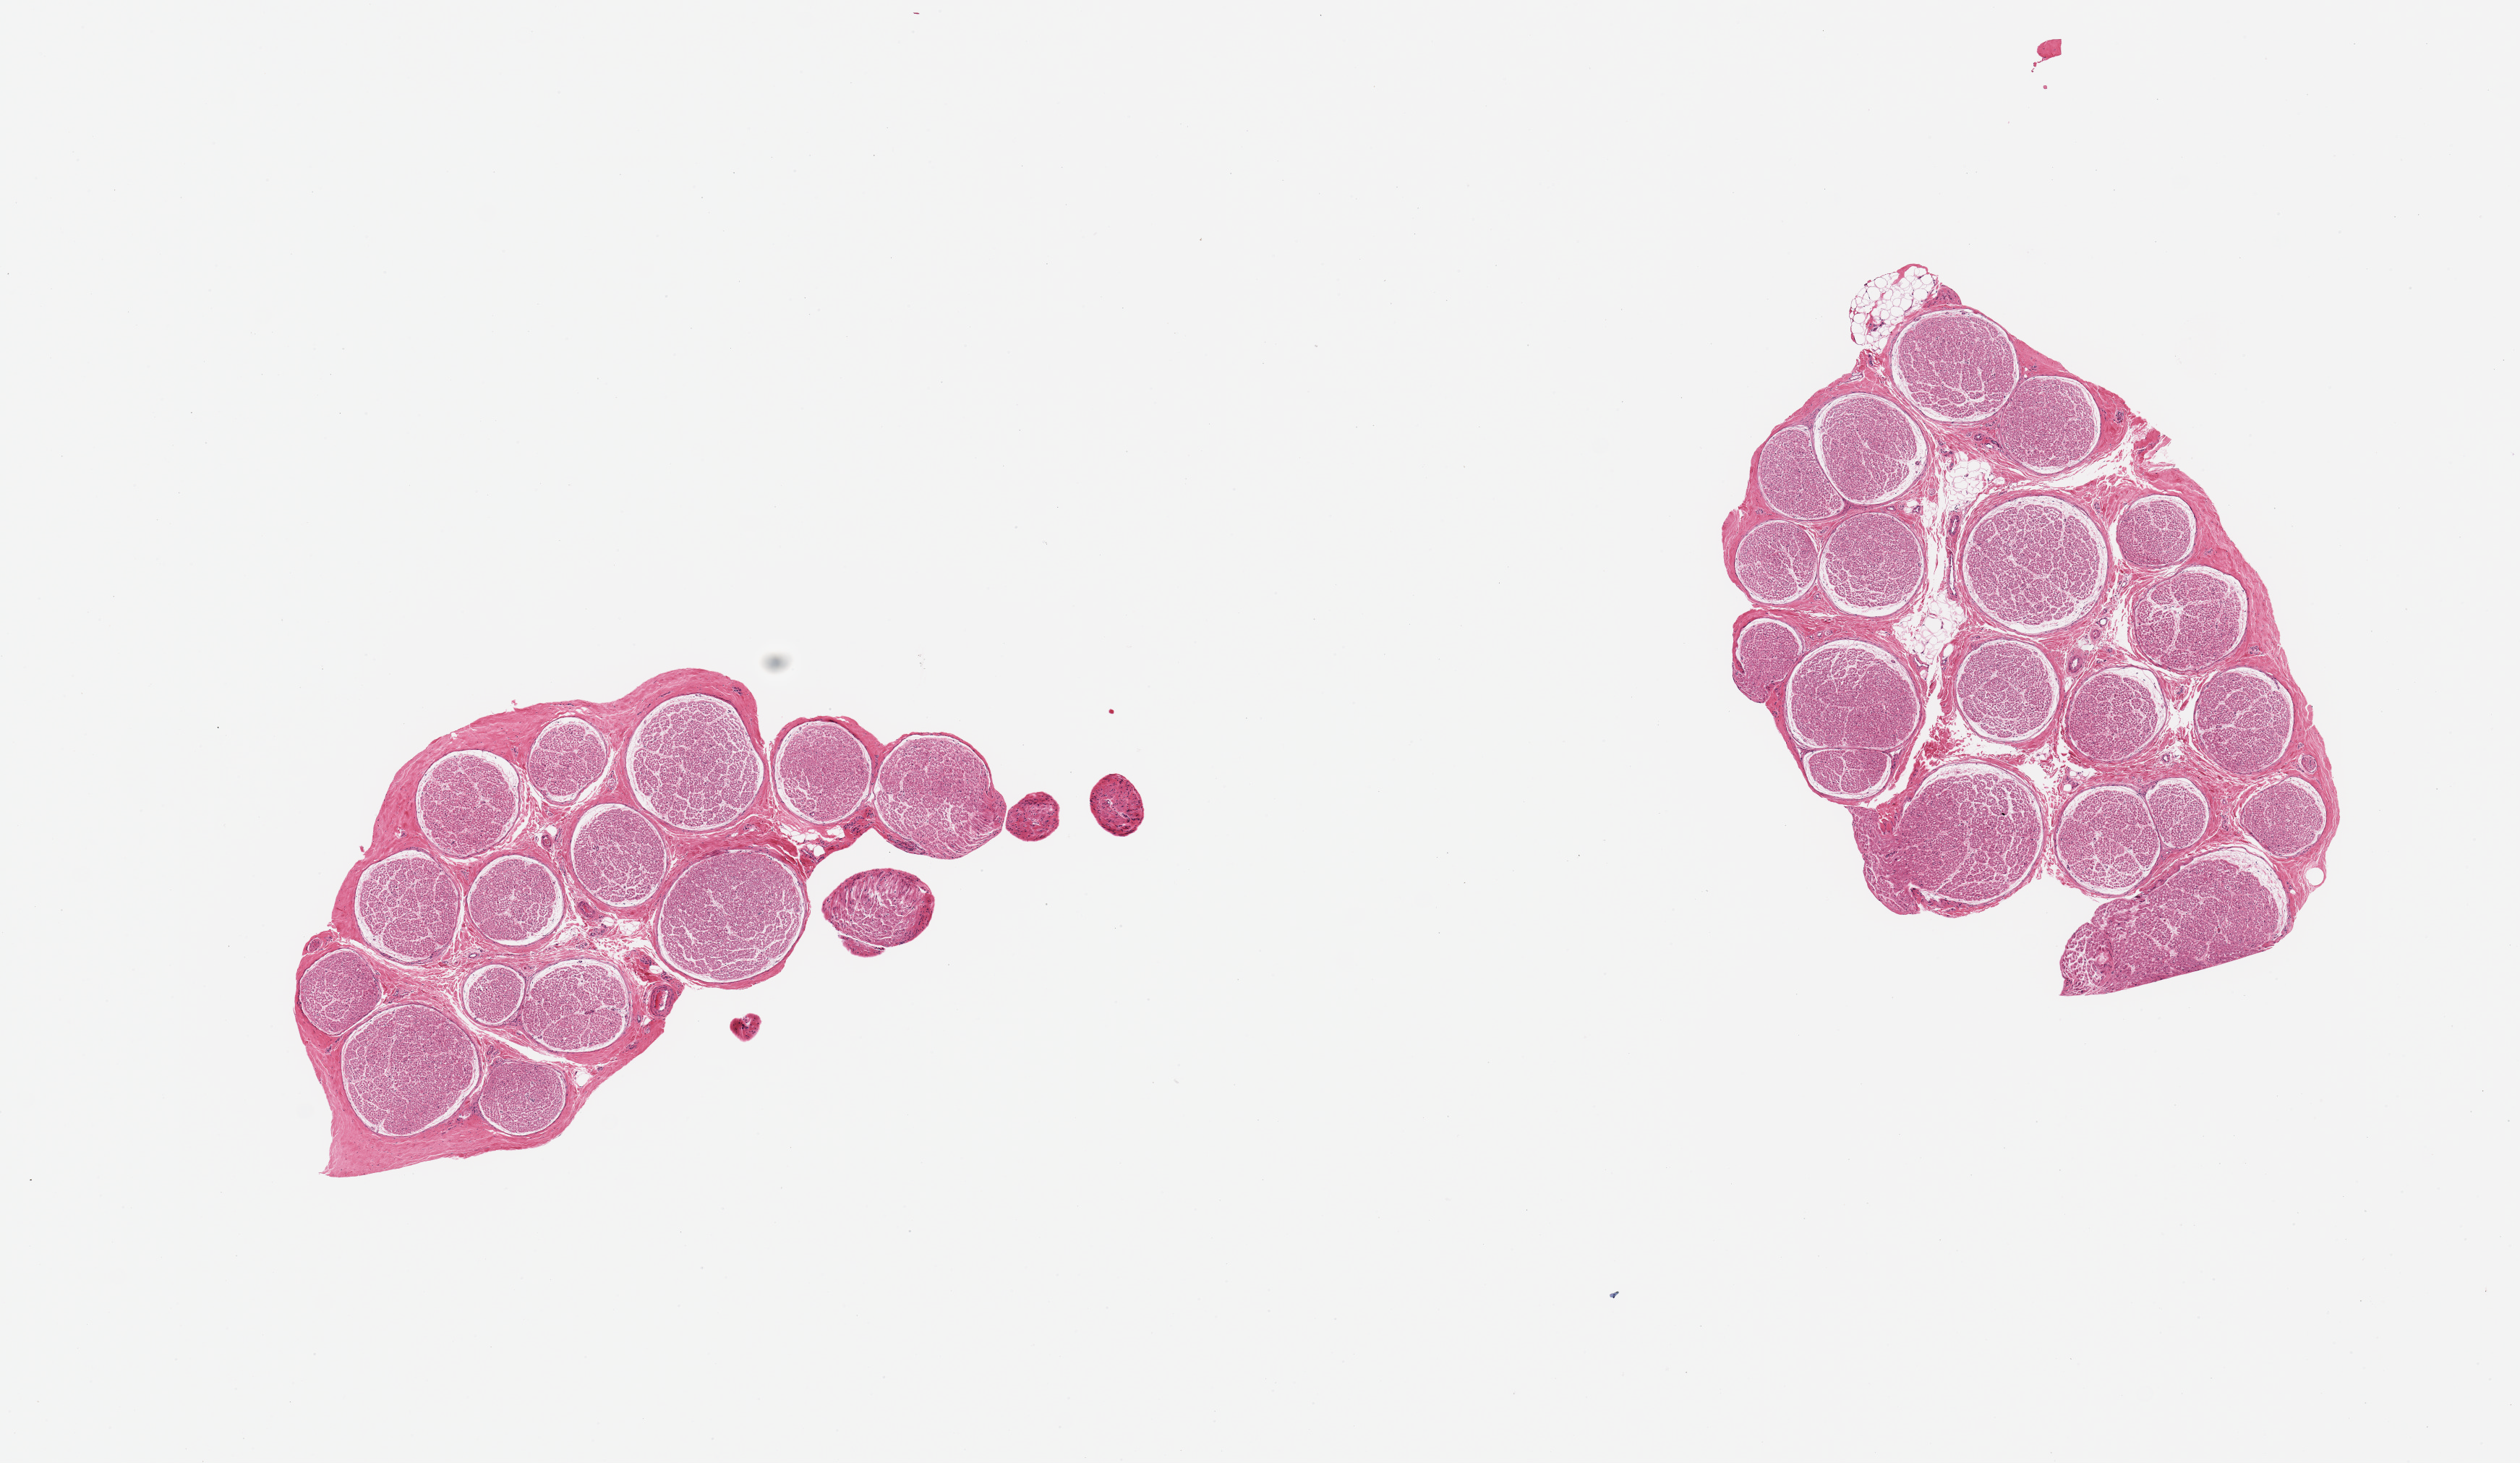
Whole-slide image, haematoxylin and eosin stain — a low-resolution overview of the entire scanned area, about 13.8 x 8.0 mm; PAXgene-fixed paraffin-embedded (PFPE) section; section of tibial nerve (target tissue); tissue donor sample.
• review note (as recorded): 2 pieces, no significant adherent fat